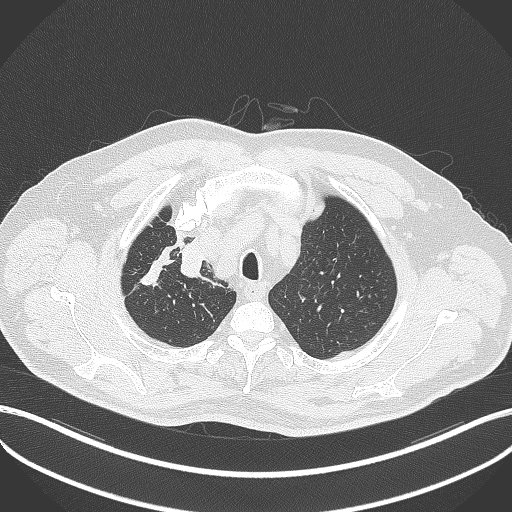
Chest CT, one axial slice; slice 325 of 411 in the series (ordered by position); reconstruction kernel B70f; lung window (W 1500 / L -600 HU); 1 mm slice thickness; 512 × 512 image matrix, field of view 400 × 400 mm. Male patient, age 60 years. Case-level facts recorded for this patient, not image findings: clinical TNM (as recorded): T1b N1 M0.
Structures marked on this image (bounding box drawn by a radiologist):
- lung tumour (recorded histology: squamous cell carcinoma): bounding box [x1, y1, x2, y2] px = [177, 234, 212, 283]